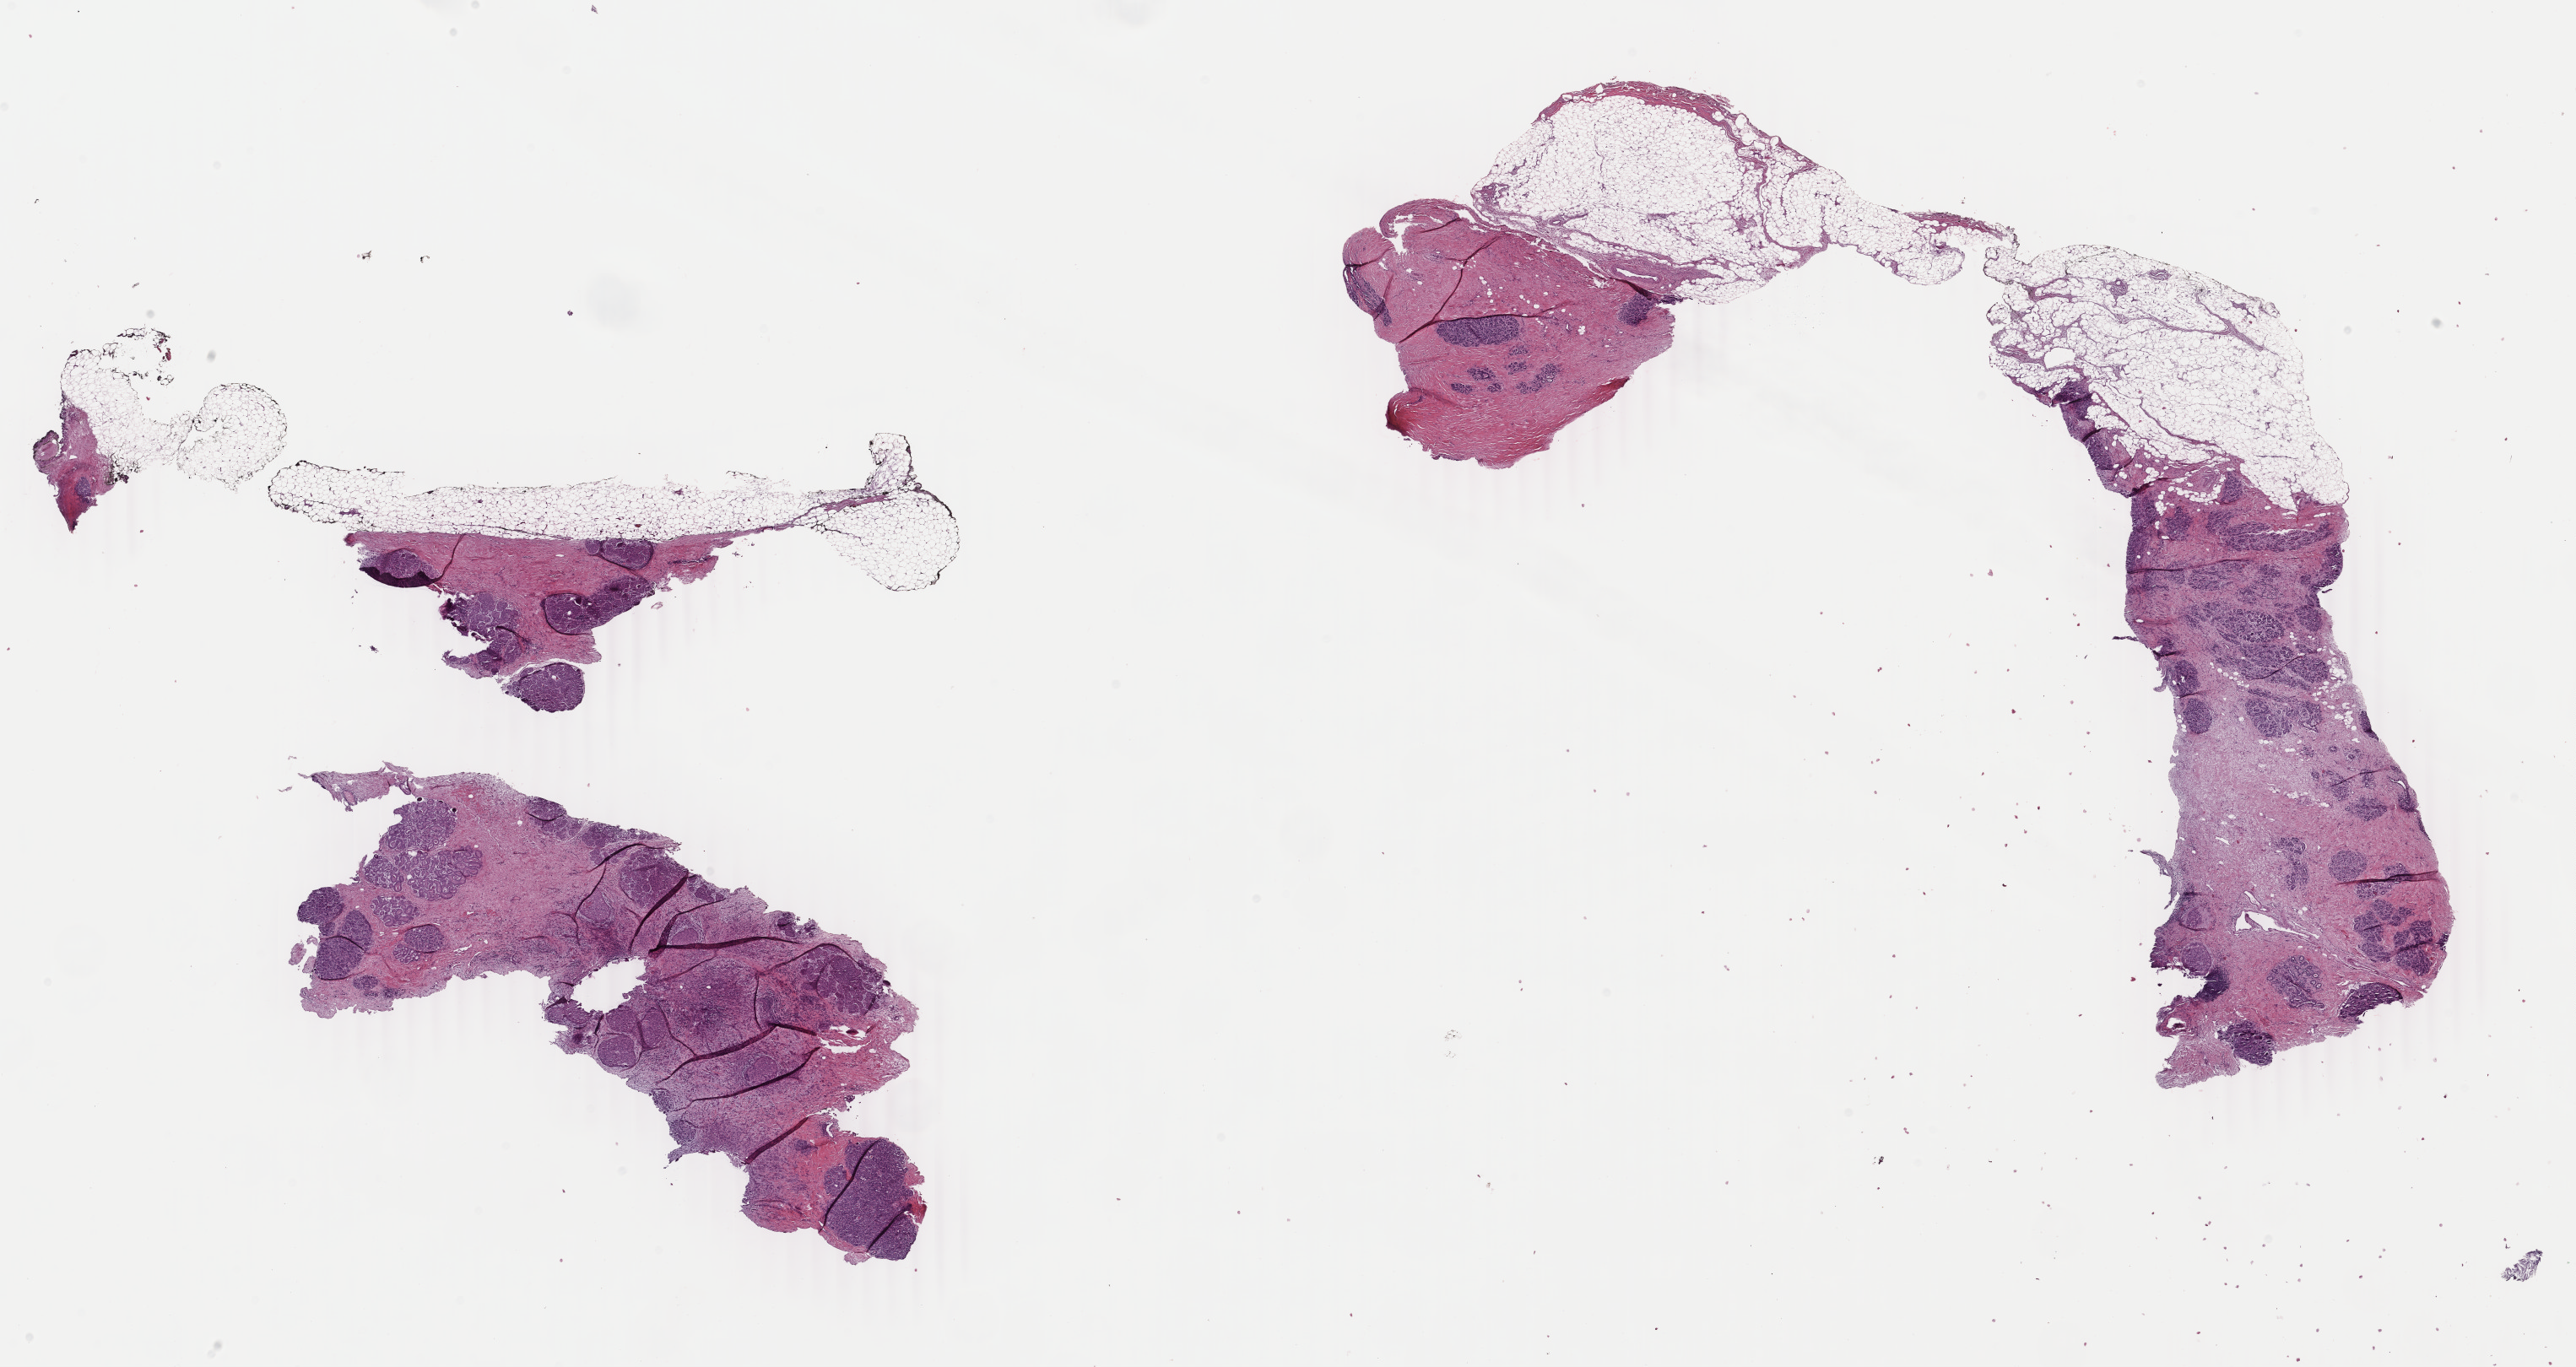
Whole-slide histology image, H&E-stained, whole scanned area (about 24.3 x 12.9 mm) shown as a low-resolution overview; formalin-fixed paraffin-embedded (FFPE) diagnostic section; breast, primary tumour sample. Patient: female, age at initial diagnosis 52 years.
Laterality: right. Lymph nodes positive (case pathology): 1 of 12 examined. AJCC pathologic stage: IIIA. Diagnosis: Lobular carcinoma, NOS.